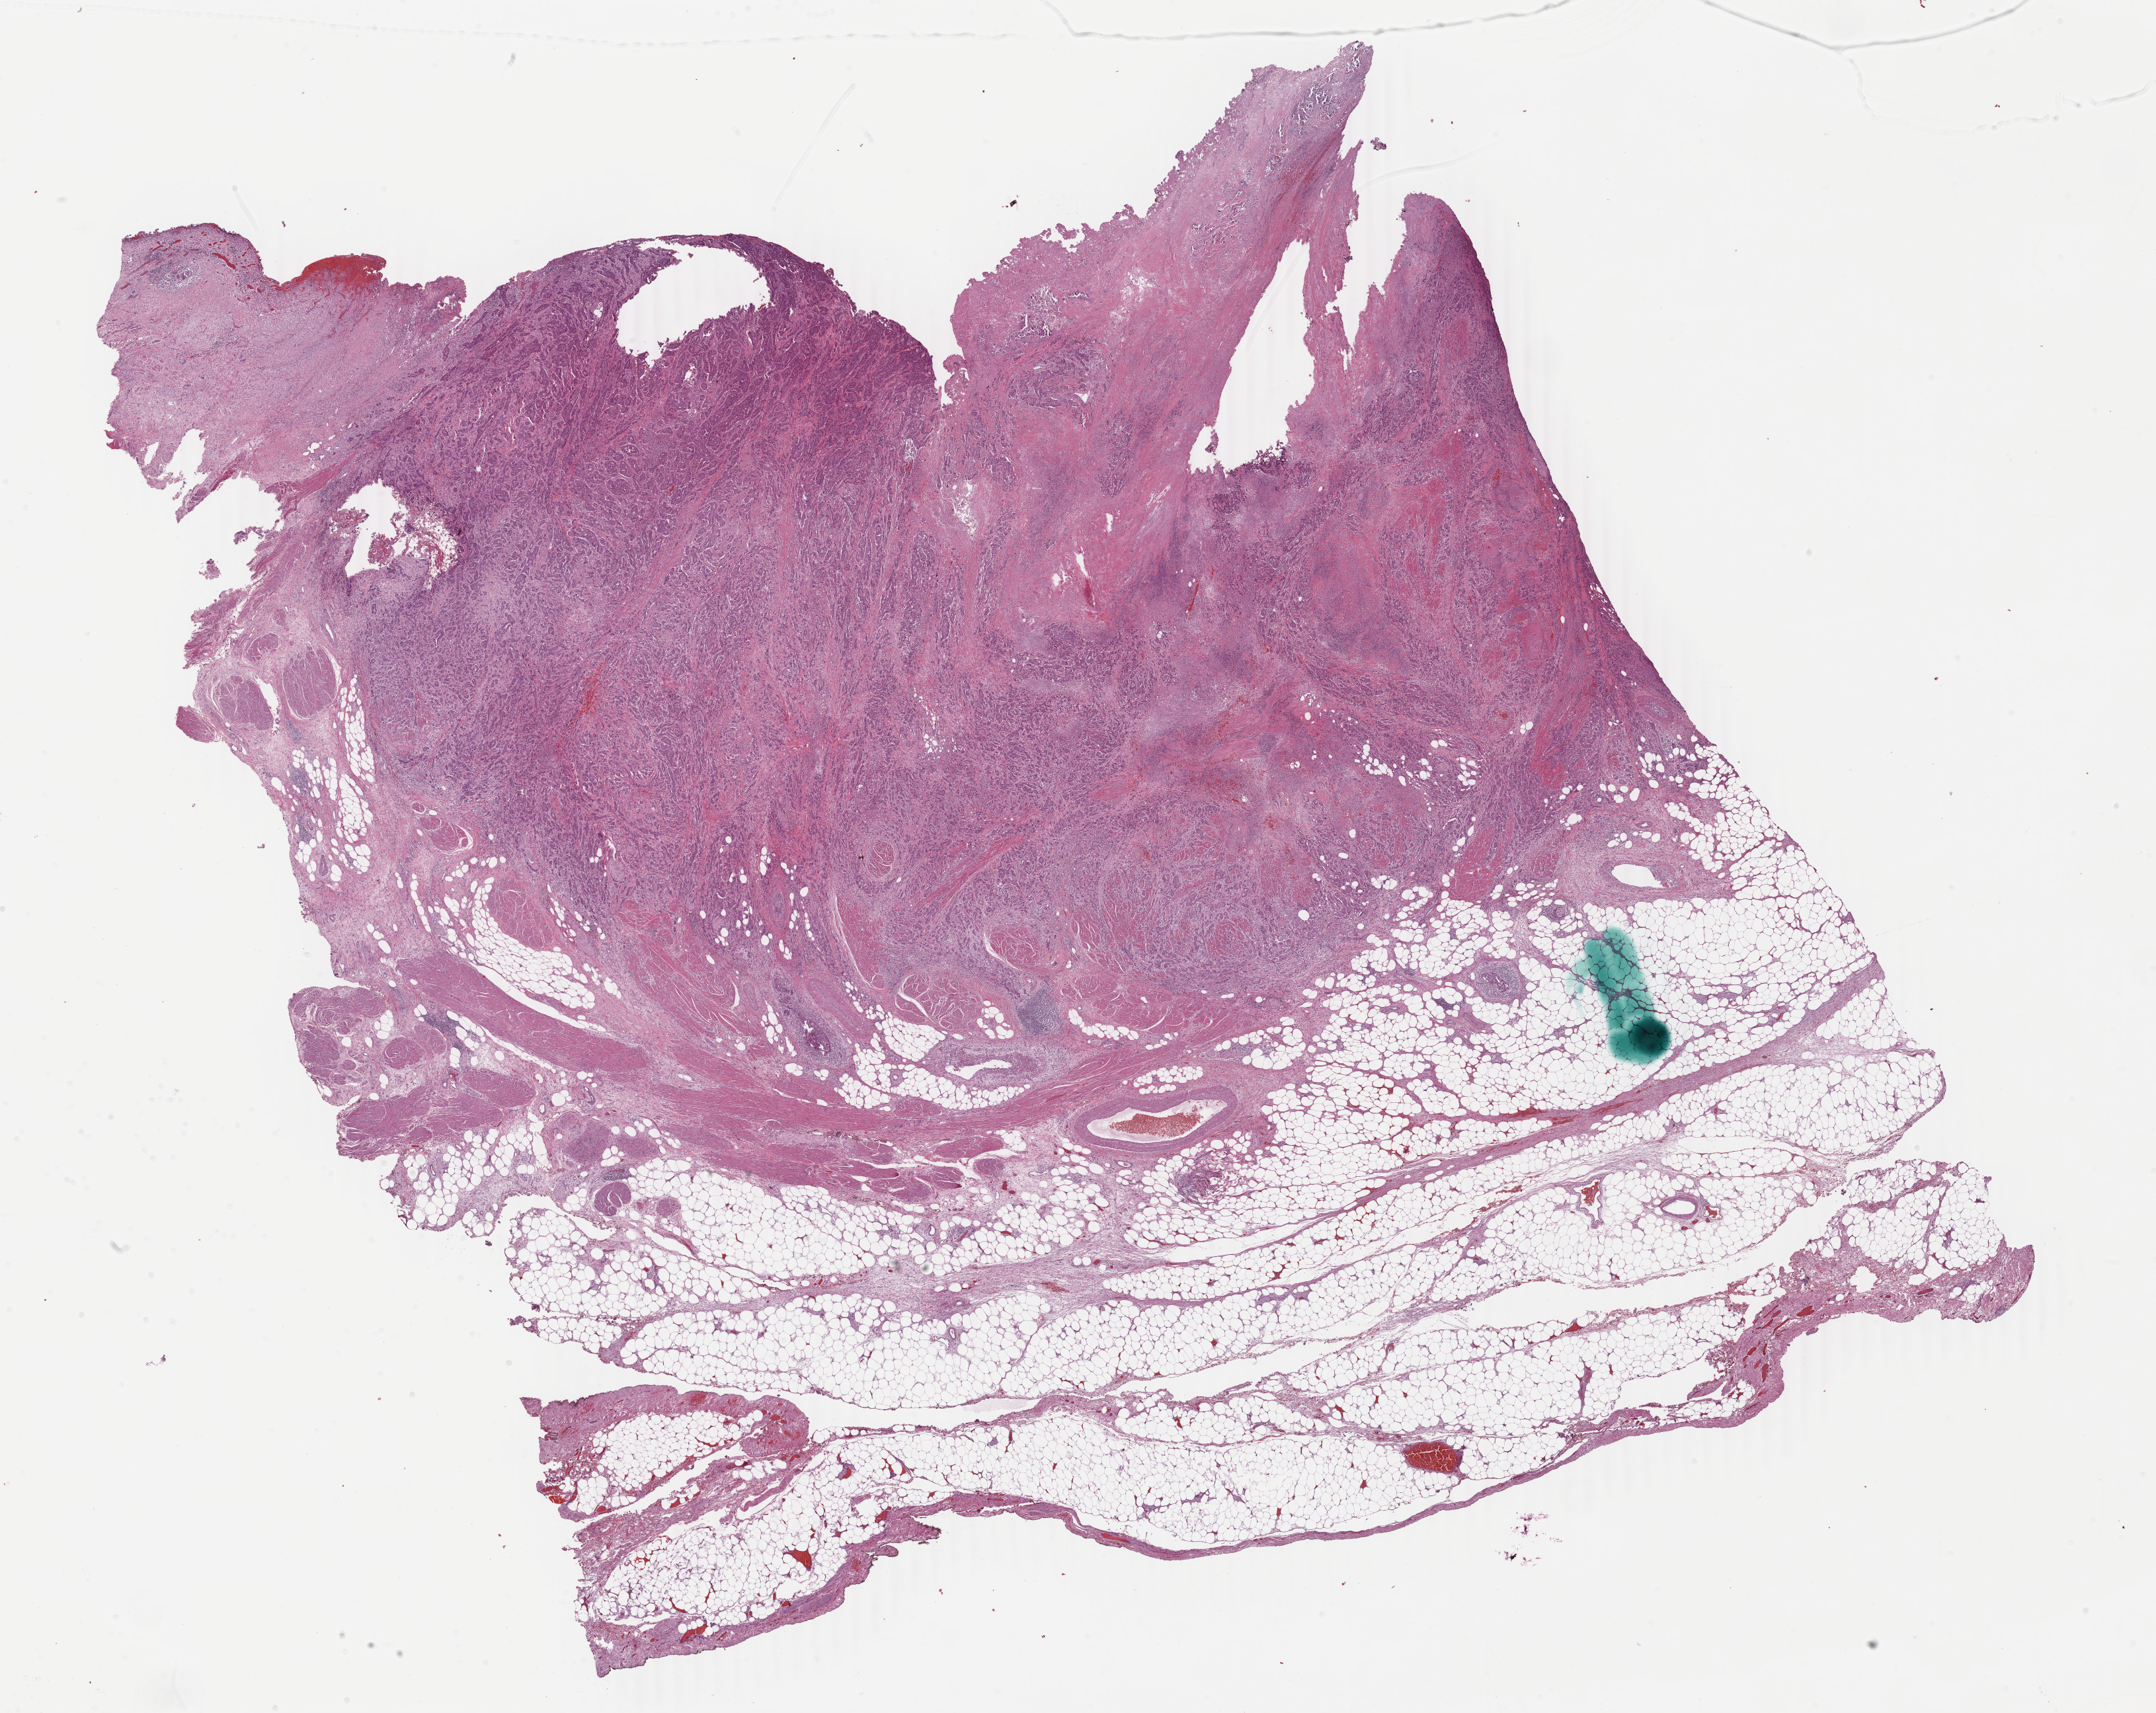
Whole-slide histology image, H&E, a low-resolution overview of the entire scanned area, about 25.9 x 20.6 mm (acquisition: 40x scan). Formalin-fixed paraffin-embedded (FFPE) diagnostic section. Primary tumour sample from the bladder. Male patient; age at initial diagnosis 76 years. Histologic grade: high grade.
Pathologic diagnosis: Transitional cell carcinoma. AJCC pathologic stage: IV (7th edition). Lymph nodes positive (case pathology): 2 of 14 examined.